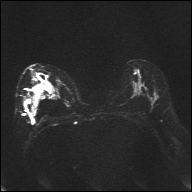
Breast MRI, one axial slice. Slice 17 of 32 in the series (ordered by position). Diffusion-weighted series; image 2 of 4 stored at this slice position (different b-values; order by instance number). 1.5 T. 4 mm slice thickness. 192 × 192 image matrix, field of view 360 × 360 mm. Female patient.
Structures marked on this image (outlined manually by an expert reader):
- tumour on diffusion-weighted imaging: bounding box [x1, y1, x2, y2] px = [34, 84, 42, 89]